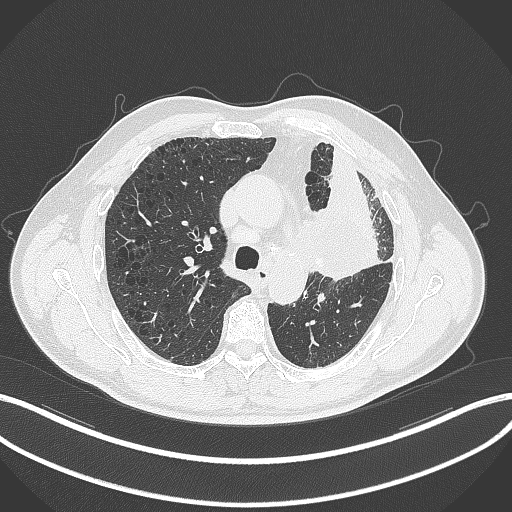
Chest CT, one axial slice. Slice 210 of 297 in the series (ordered by position). Reconstruction kernel B70f. Lung window (W 1500 / L -600 HU). 1 mm slice thickness. 512 × 512 image matrix. Male patient, age 68 years. Case-level facts recorded for this patient, not image findings: clinical TNM (as recorded): T3 N3 M1.
Outlined on this slice (bounding box drawn by a radiologist):
- lung tumour (recorded histology: adenocarcinoma): bounding box <308,189,377,282> (left, top, right, bottom; pixels)